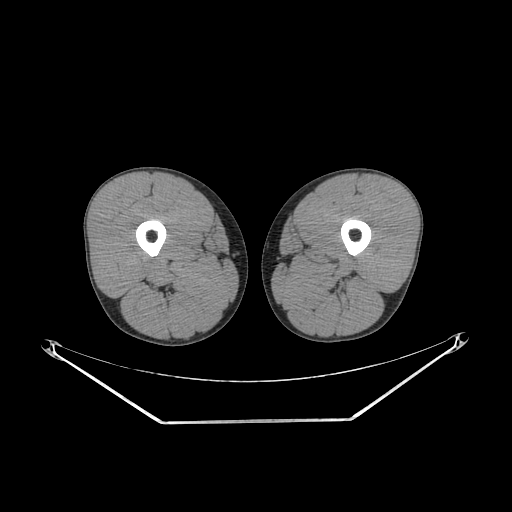
CT of an extremity soft-tissue mass (from a PET/CT study), one axial slice. Slice 221 of 267 in the series (ordered by position). Reconstruction kernel SOFT. 140 kVp. Soft-tissue window (W 400 / L 40 HU). 3.75 mm slice thickness. 512 × 512 image matrix, field of view 500 × 500 mm. Male patient. From the clinical record (not read from this slice): histological type: extraskeletal osteosarcoma; grade: high; site of the primary tumour: left adductur.
Structures marked on this image (expert contour drawn on MRI and transferred to this co-registered scan by the dataset authors):
- gross tumour volume (mass): bounding box (x1, y1, x2, y2) in pixels: (283, 249, 359, 280)